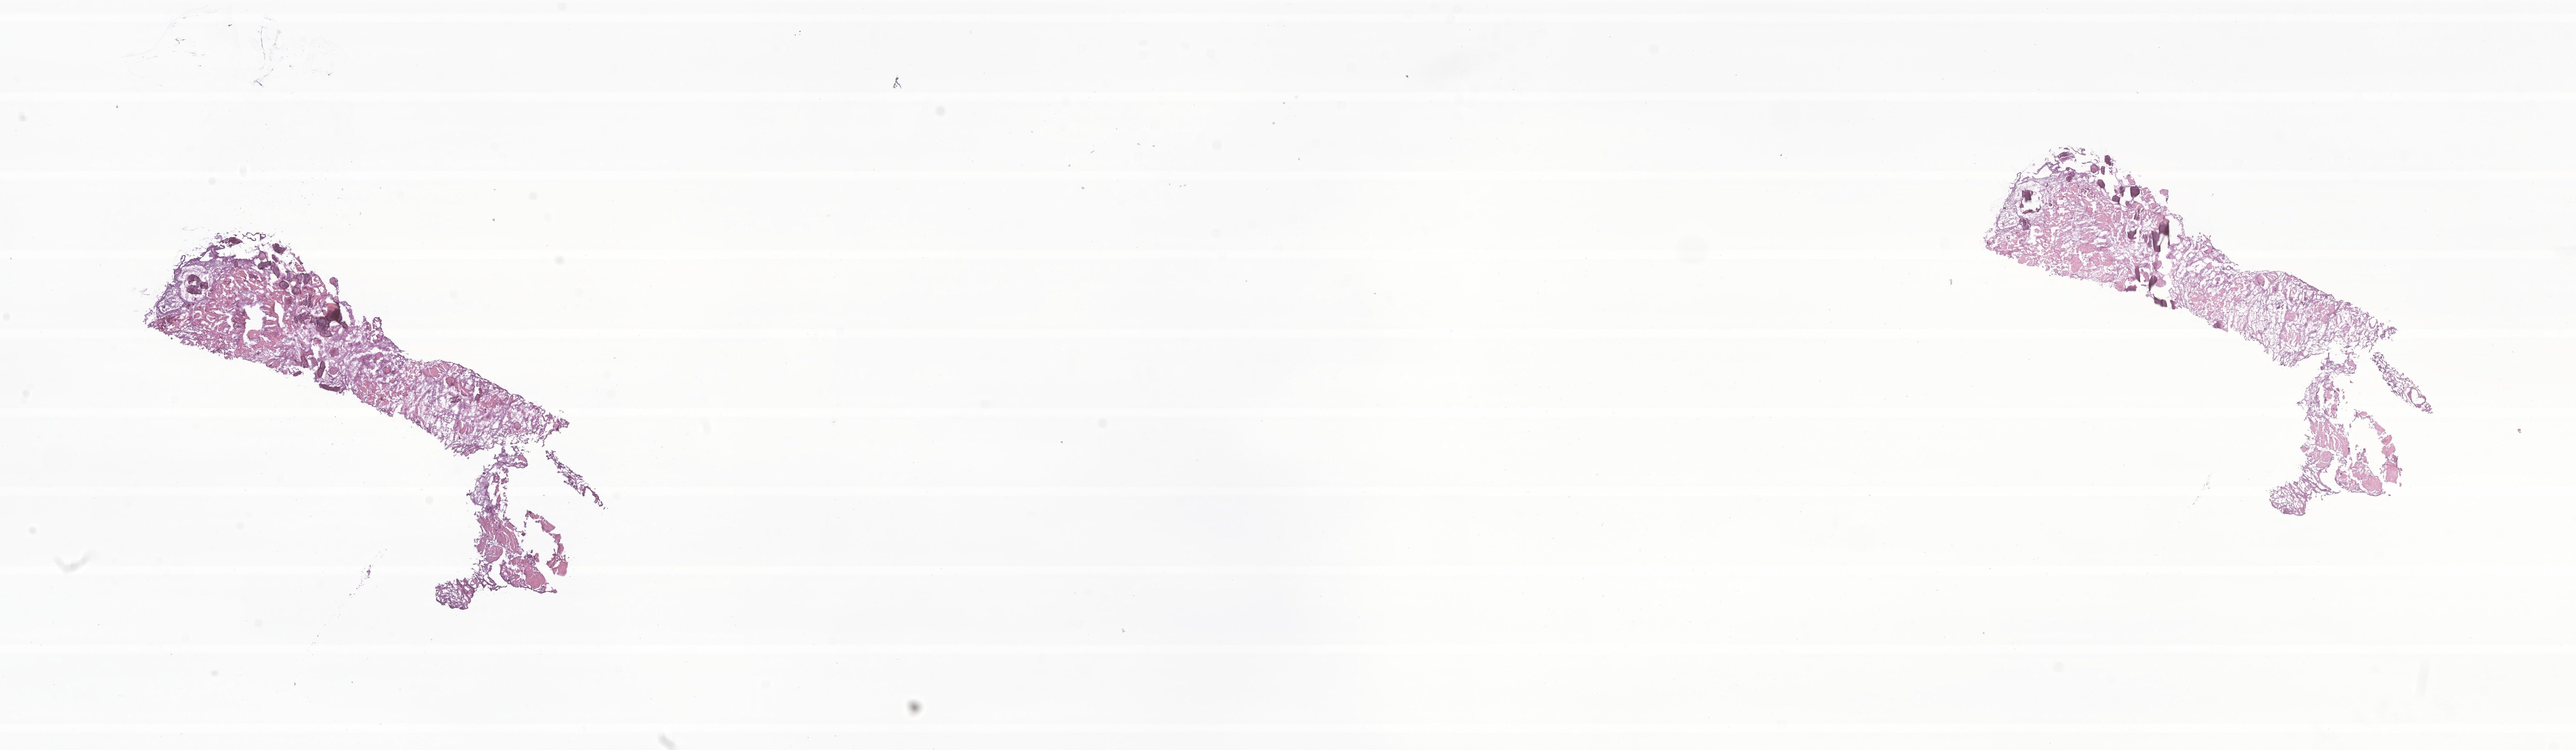
Haematoxylin and eosin whole-slide image of tumor tissue from the brain — low-resolution overview of the scanned area, about 34.9 x 10.1 mm, frozen section (OCT-embedded). Patient female; age 200 months.
Recorded diagnosis: Craniopharyngioma, NOS.